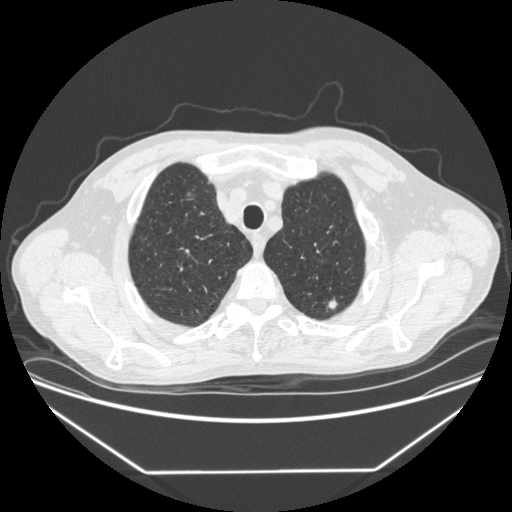
Low-dose screening chest CT, one axial slice. Slice 334 of 383 in the series (ordered by position). Reconstruction kernel STANDARD. 120 kVp. Lung window (W 1500 / L -600 HU). 512 × 512 image matrix, field of view 418 × 418 mm.
Structures marked on this image (outlined manually by an expert reader):
- lesion 1 (tumor, upper lobe of left lung): bounding box [x1, y1, x2, y2] px = [327, 298, 338, 309]